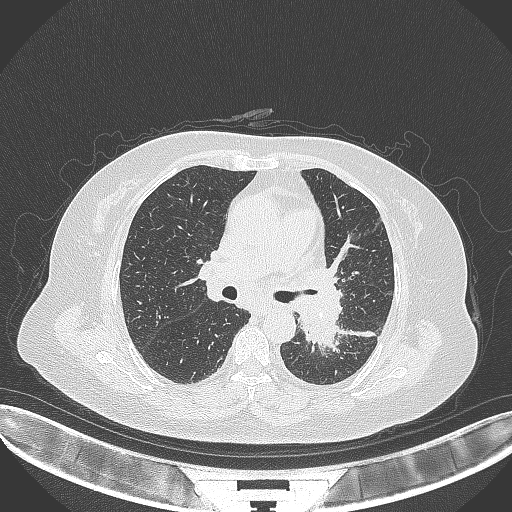
Chest CT, one axial slice; slice 204 of 322 in the series (ordered by position); reconstruction kernel B70f; lung window (W 1500 / L -600 HU); 512 × 512 image matrix. Female patient, age 69 years. Case-level facts recorded for this patient, not image findings: clinical TNM (as recorded): T2b N3 M1.
Annotated regions visible in this slice (rectangle marked by the reading radiologist):
- lung tumour (recorded histology: adenocarcinoma): bounding box <296,294,342,355> (left, top, right, bottom; pixels)